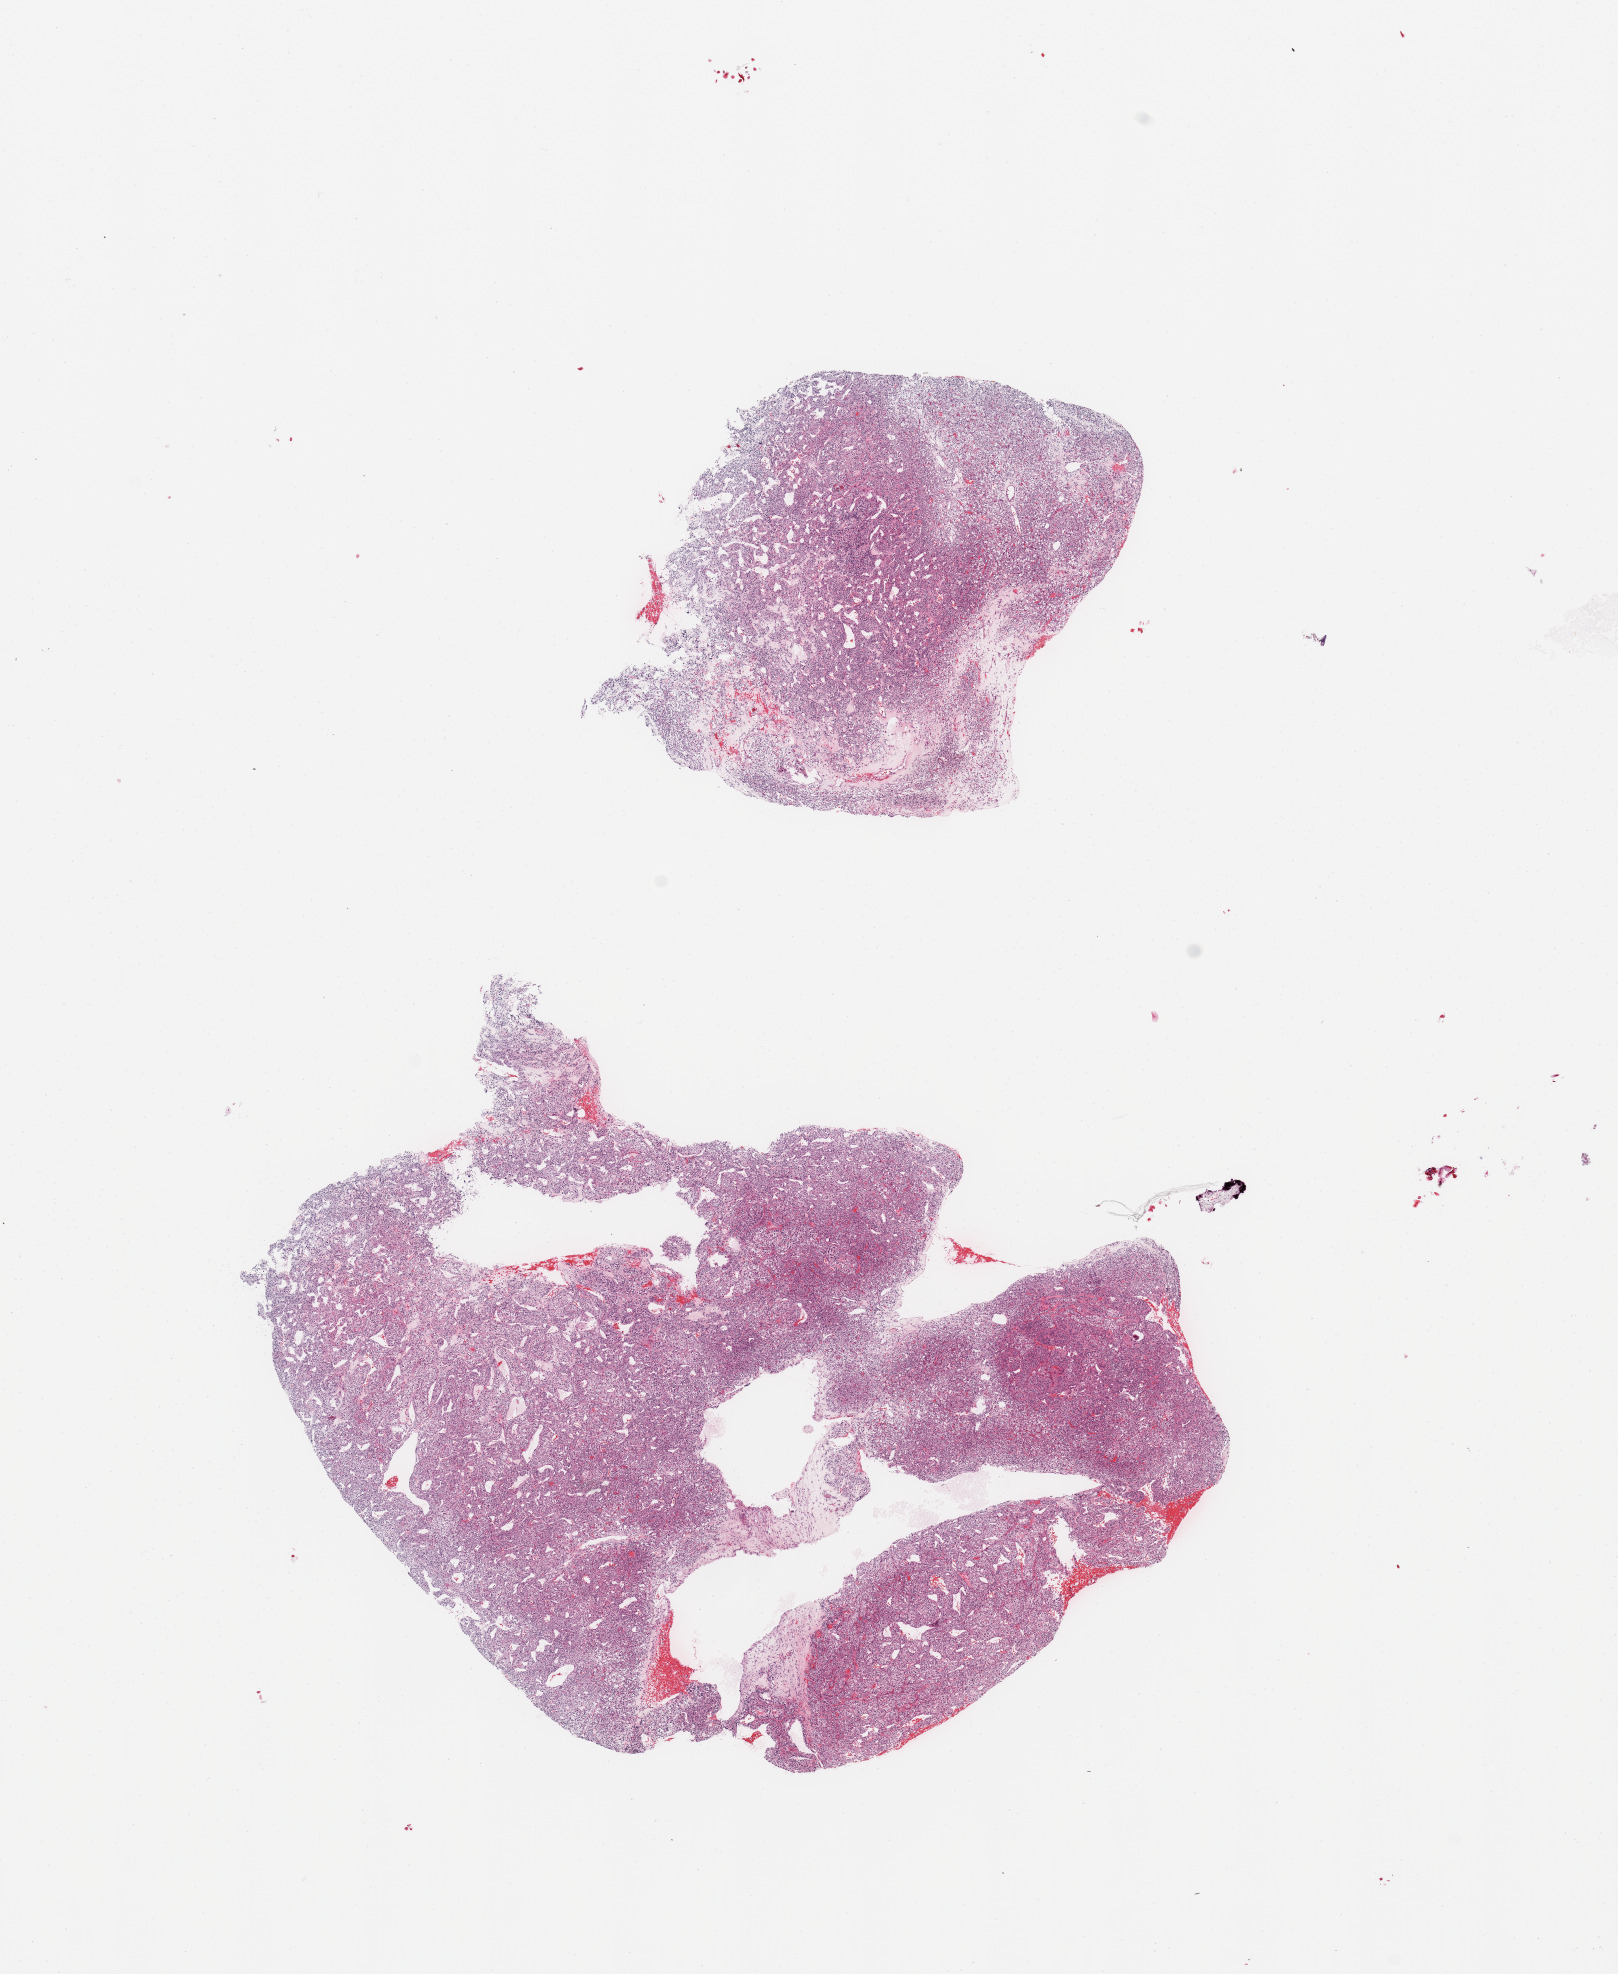
H&E whole-slide image — low-resolution overview of the scanned area, about 12.8 x 15.6 mm. Tumour tissue sample, sampled site: kidney. Patient: male, age 89 years. Histologic grade: G2 (moderately differentiated). Composition of this section per pathologist review: tumour nuclei 90%, necrosis 0%.
Primary tumour site (as recorded): lower pole. Histologic diagnosis: Renal cell carcinoma, NOS. AJCC pathologic stage: III.